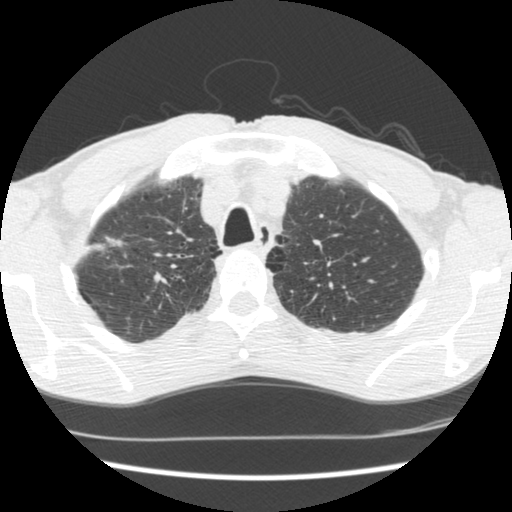
Chest CT (low-dose screening protocol), one axial image, first (baseline) screen, lung window (W 1500 / L -600 HU), 2.5 mm slice thickness, standard (soft-tissue) reconstruction kernel (STANDARD), slice 40 of 197 in the series. Male, age 62 years at enrolment.
• Lesion marked by an expert reader, bounding box [x1, y1, x2, y2] px = [76, 219, 131, 274].
• No non-calcified nodule or mass ≥4 mm was recorded by the screening reader at this exam.
• Lung cancer was diagnosed 640 days after this screen (after the second annual screen): adenocarcinoma, NOS, right upper lobe, poorly differentiated (G3), stage IIA (AJCC 6th edition), 22 mm at pathology.